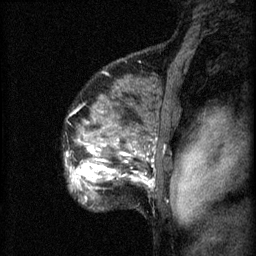
Breast MRI (dynamic contrast-enhanced), one sagittal slice. Position 50 of 60 along the scan axis. 3 images stored at this slice position (order not interpretable as contrast timing). 1.5 T. TE 4.2 ms, TR 8.2 ms. 2 mm slice thickness. 256 × 256 image matrix, field of view 180 × 180 mm. Patient: female, 48 years.
Outlined on this slice (semi-automatically segmented with operator editing):
- analysis volume of interest (the breast-tissue region the enhancement analysis was run in; not a lesion): bounding box (x1, y1, x2, y2) in pixels: (66, 138, 153, 201)
- tumour enhancement mask (voxels above the 70 % enhancement threshold inside the analysis volume of interest): (69, 160, 152, 199)